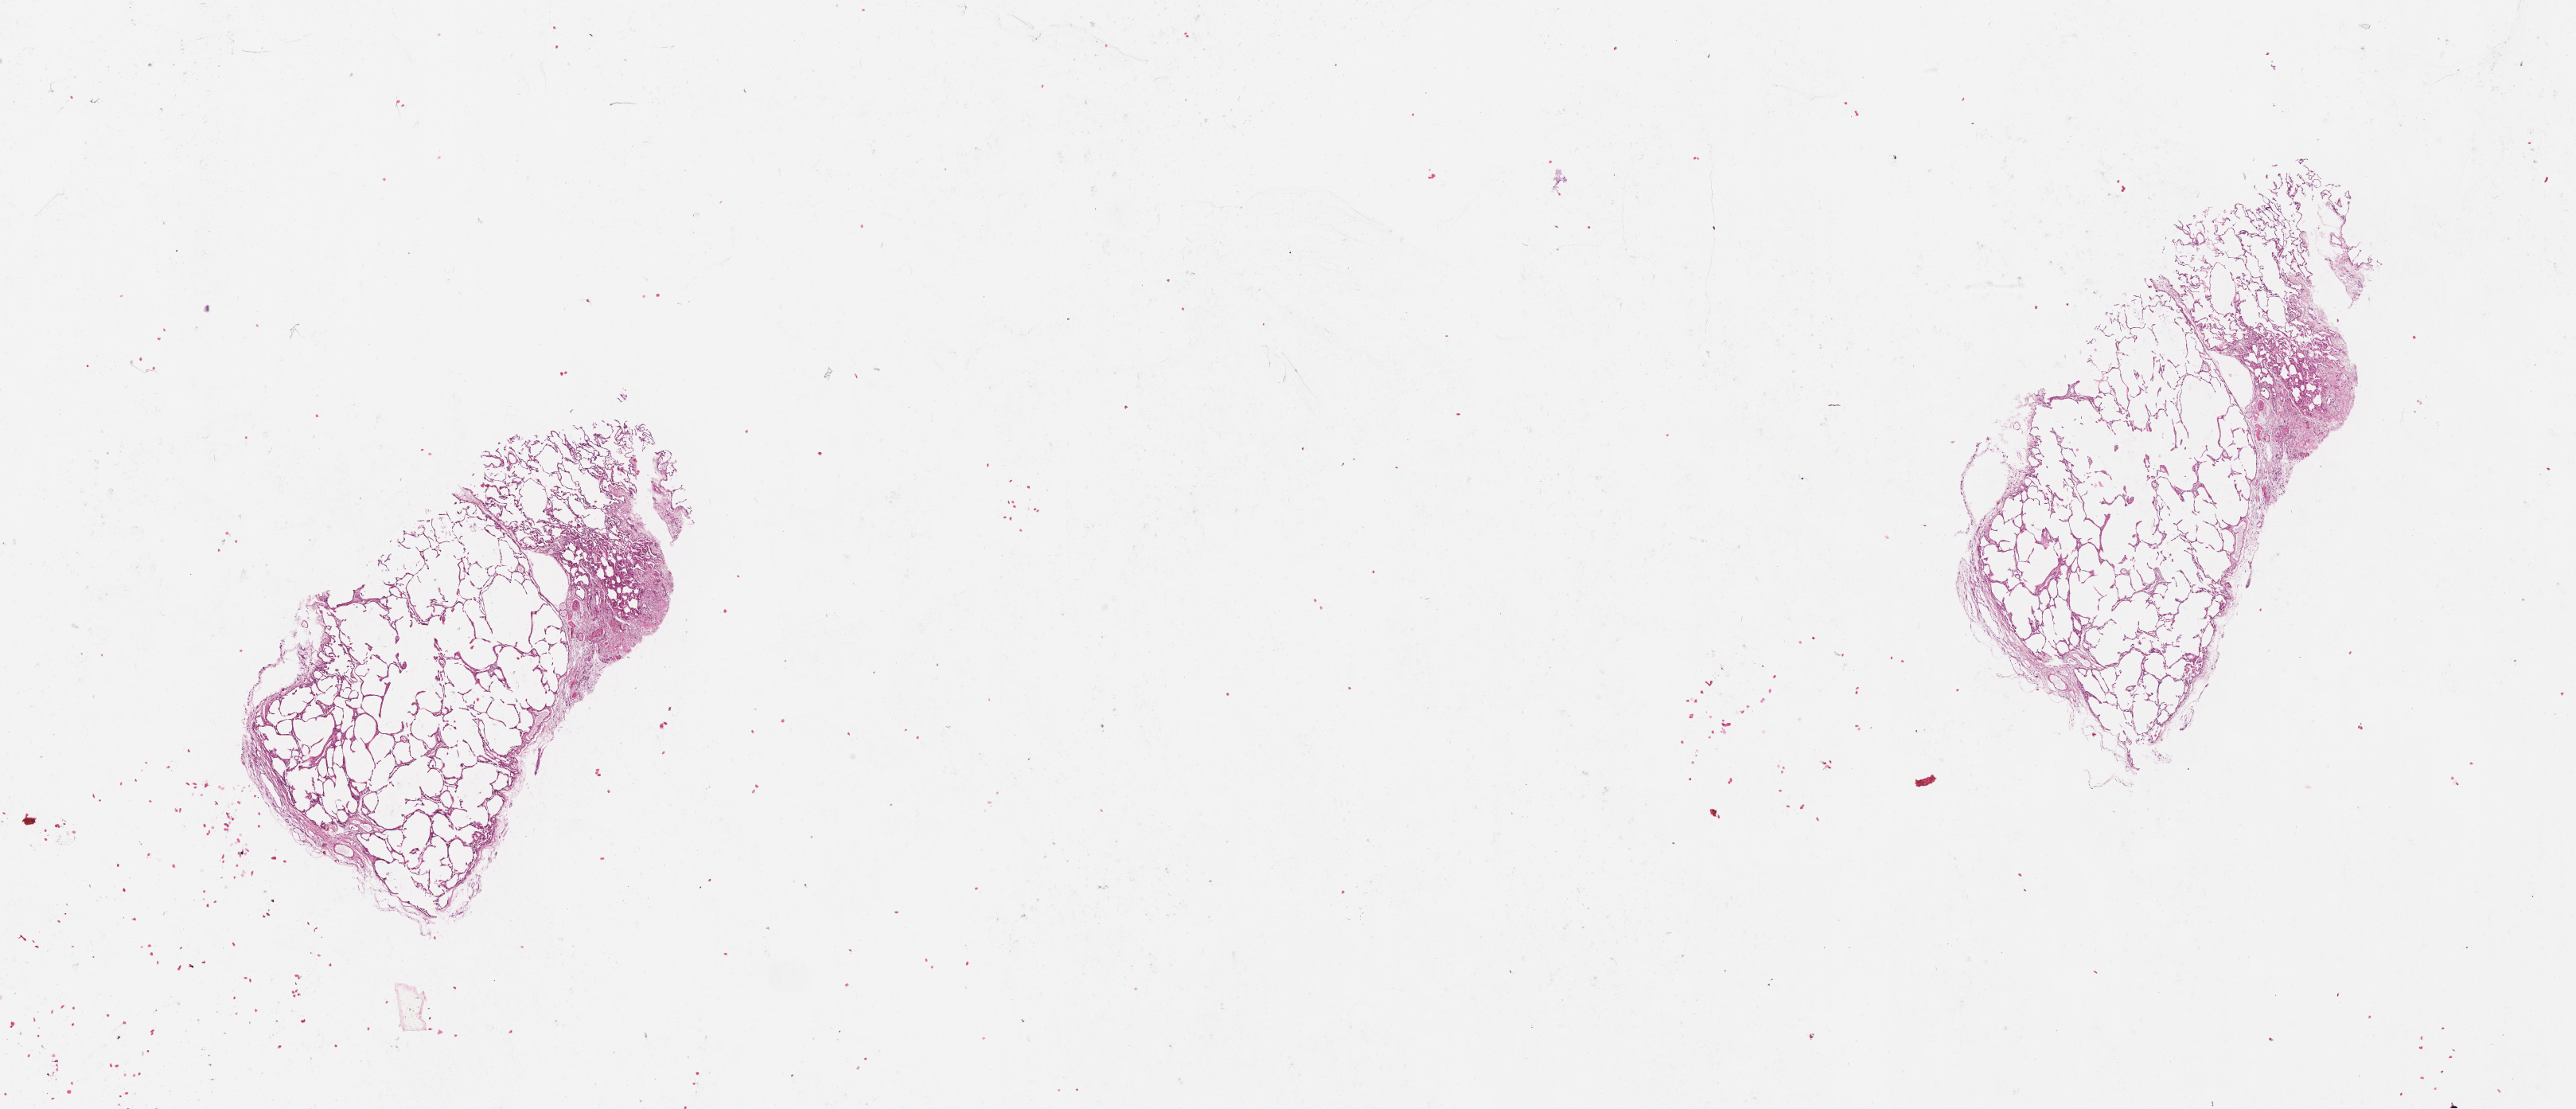
H&E-stained whole-slide image, shown as a low-resolution overview of the whole scanned area (about 26.1 x 11.2 mm, acquisition: 20x scan), lung, normal (non-tumour) tissue. 74-year-old female patient.
This section: normal (non-tumour) tissue from the same patient. Patient diagnosis (cohort enrolment): squamous cell carcinoma (lung).